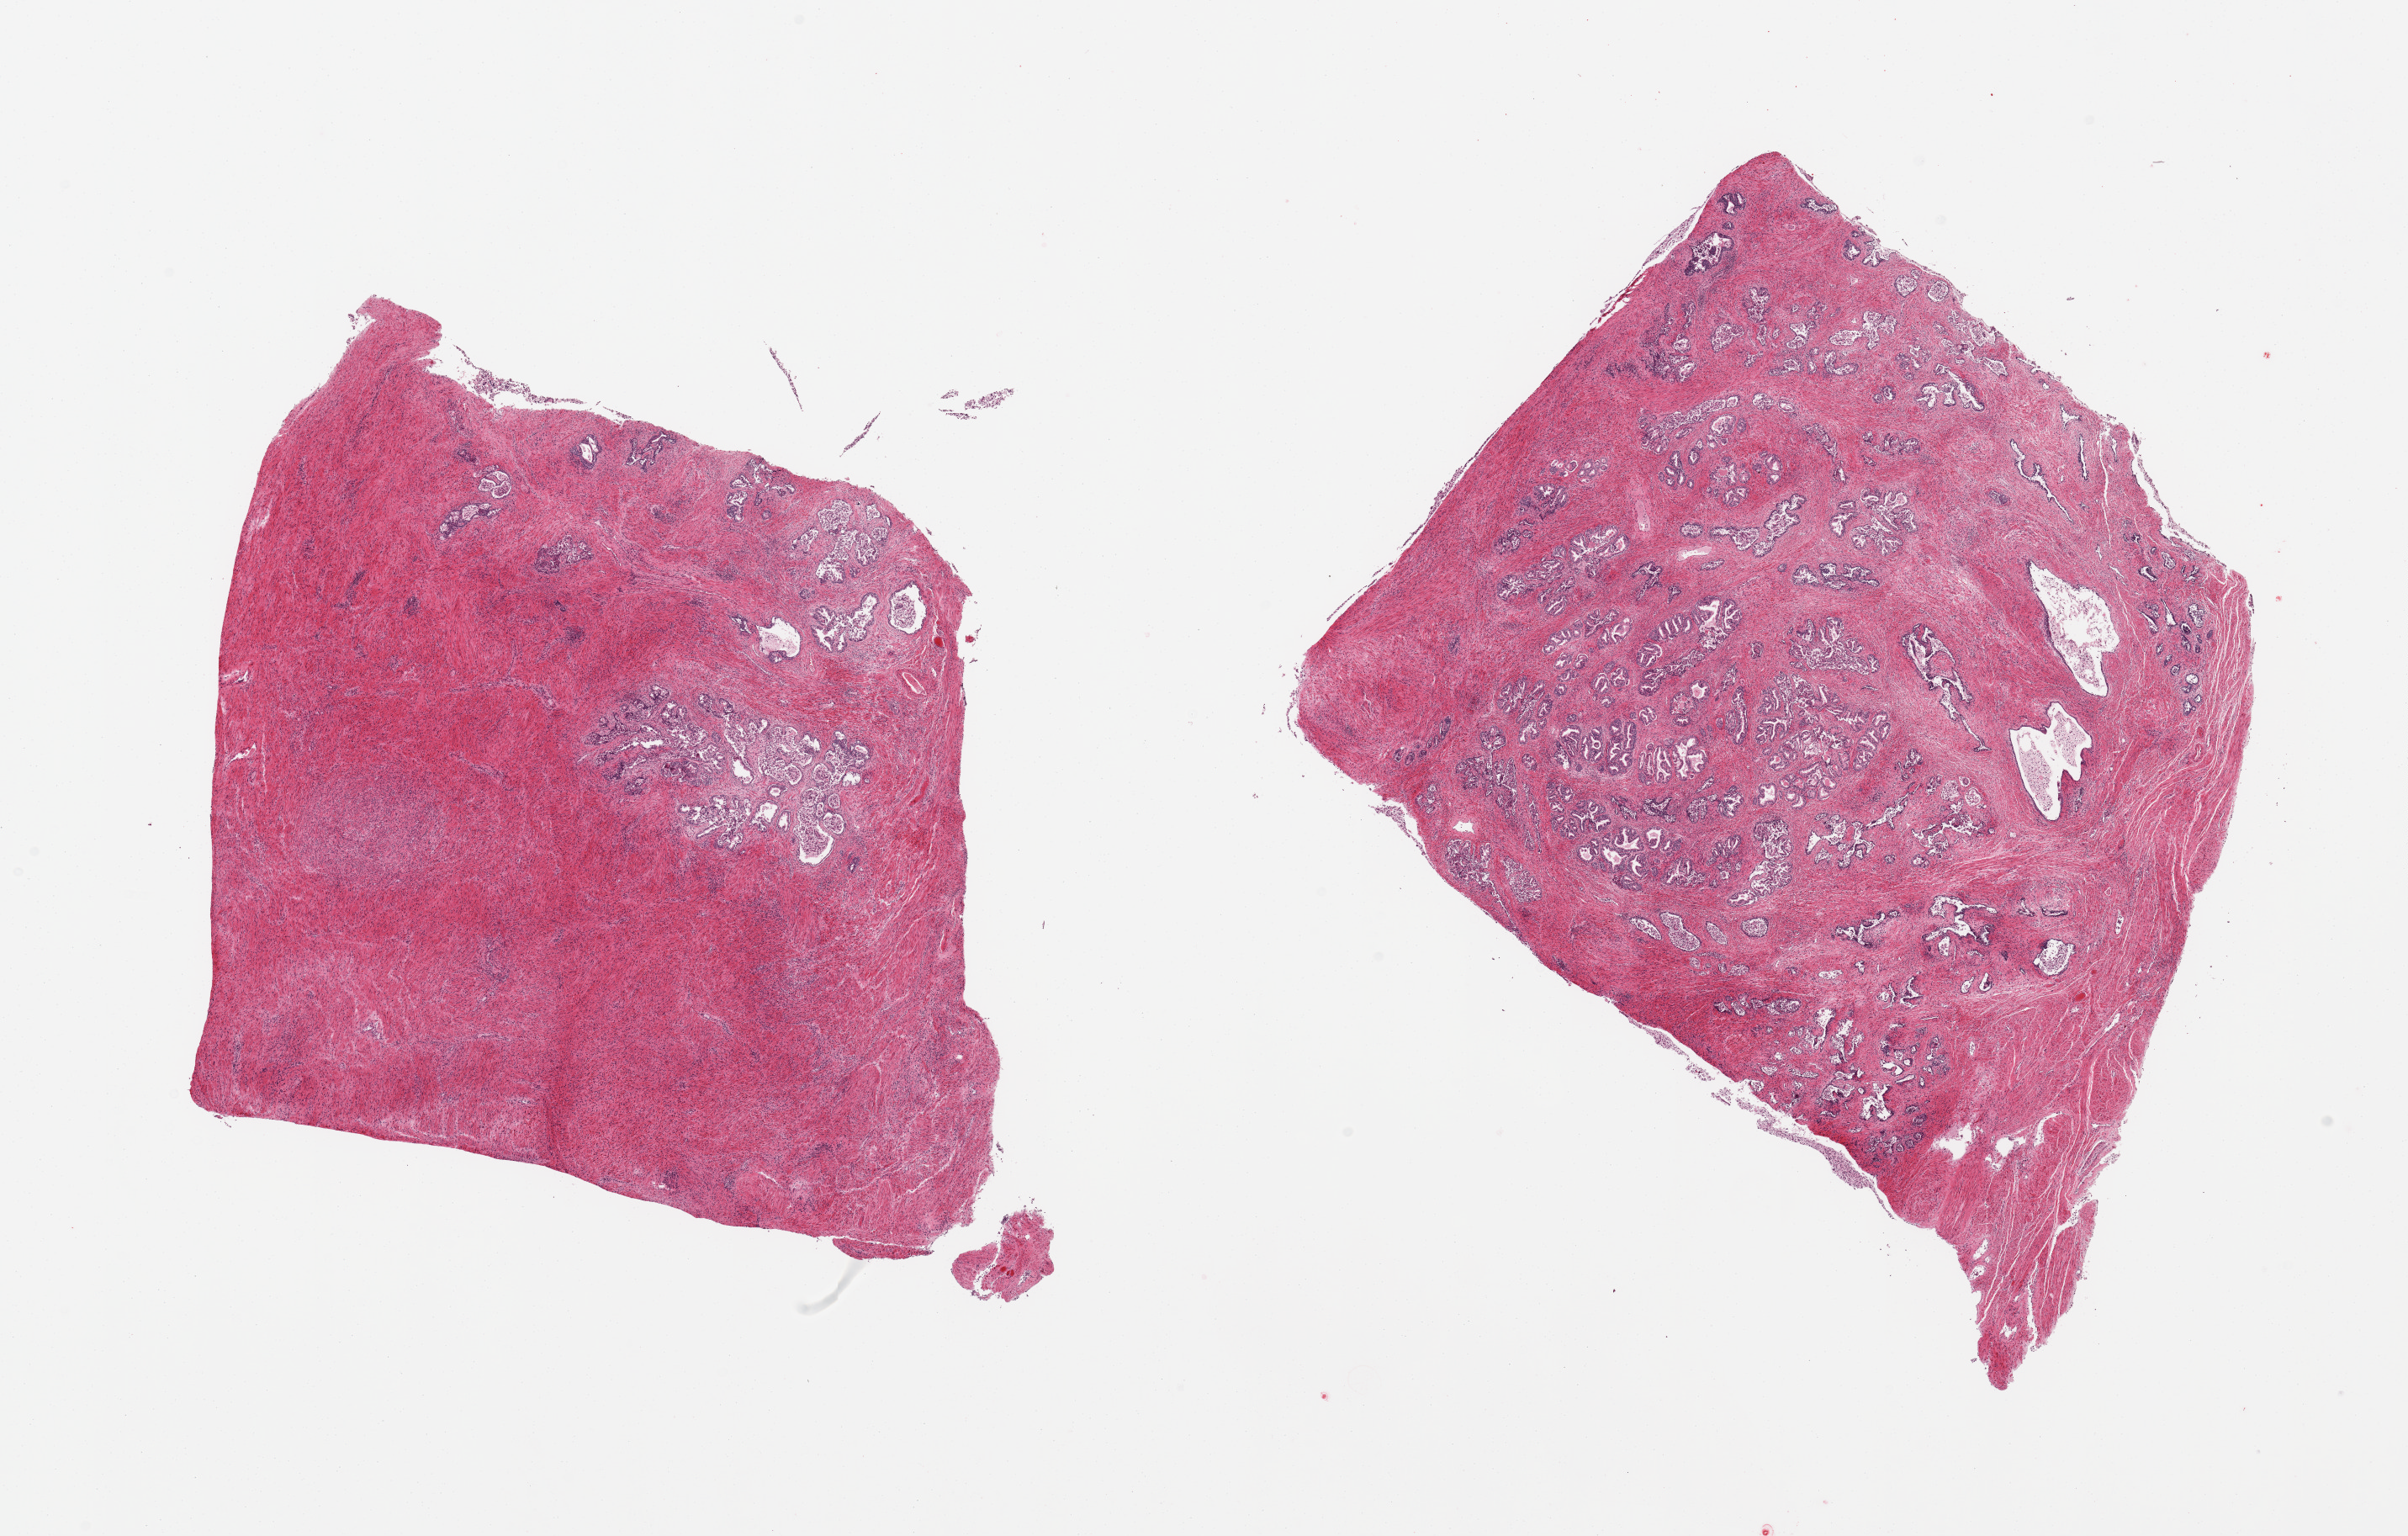
Digitized H&E-stained section, low-resolution overview of the scanned area, about 22.6 x 14.4 mm, PAXgene-fixed paraffin-embedded (PFPE) section, target tissue: prostate, tissue donor sample. Male donor.
Pathologist's review note for this sample: 2 pieces; 1 piece has plenty of glands, rather well preserved; other is largely stroma with more gland autolysis.